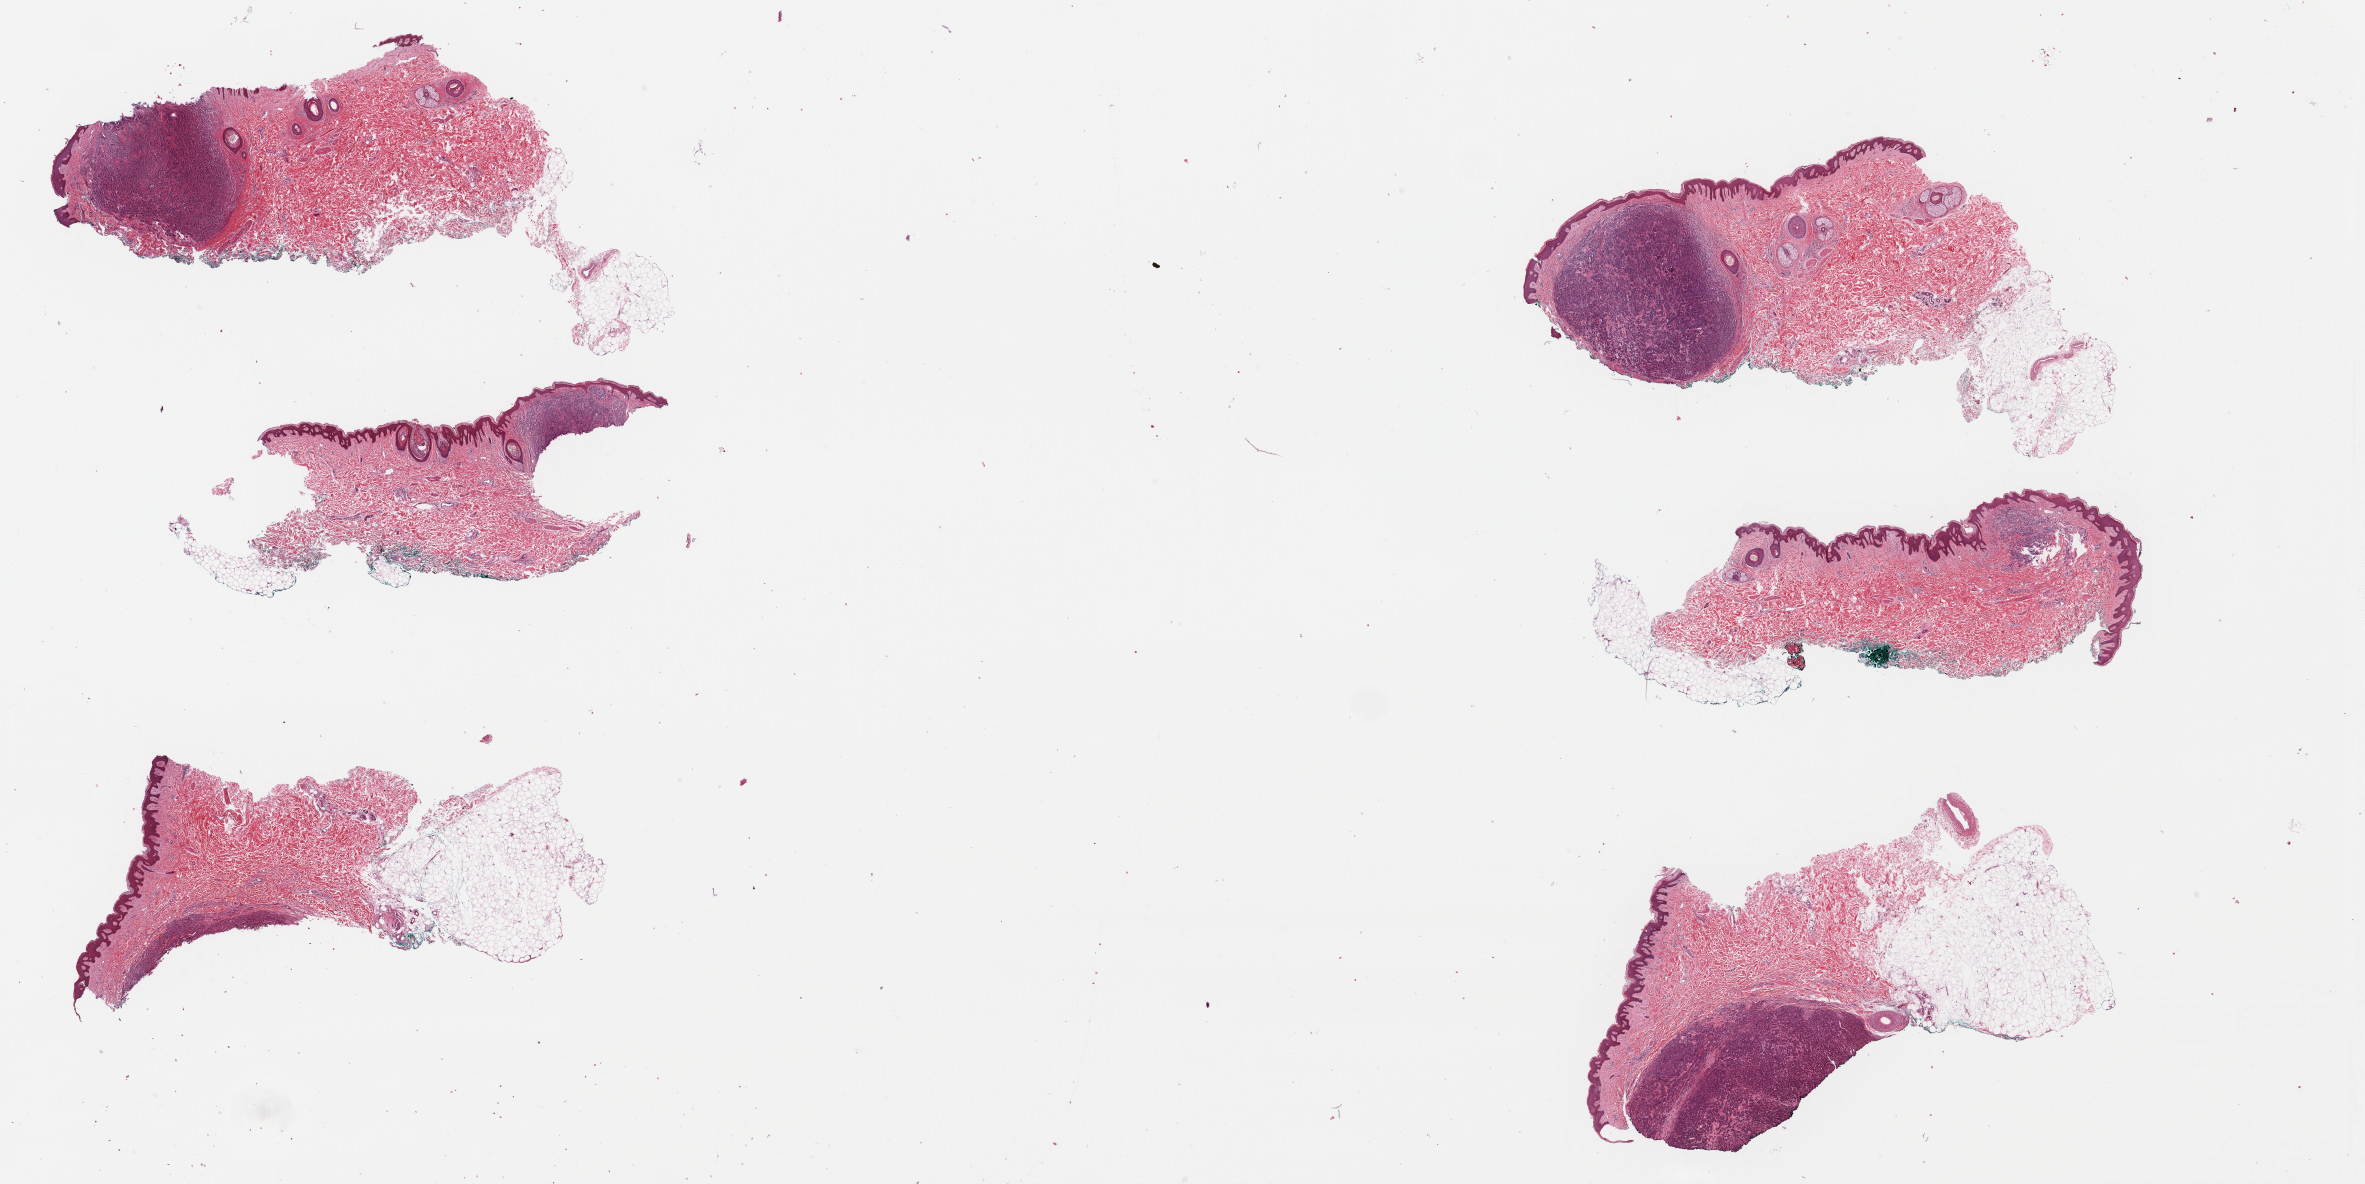
Digitized Hematoxylin and eosin (H&E) stained tissue section (whole slide) — low-resolution overview of the scanned area, about 37.2 x 18.6 mm (from a 40x scan). Formalin-fixed paraffin-embedded (FFPE) diagnostic section. Metastatic tumour sample, sampled site not recorded. Male patient; age at initial diagnosis 40 years.
- this section: metastatic tumour tissue
- patient diagnosis: Malignant melanoma, NOS